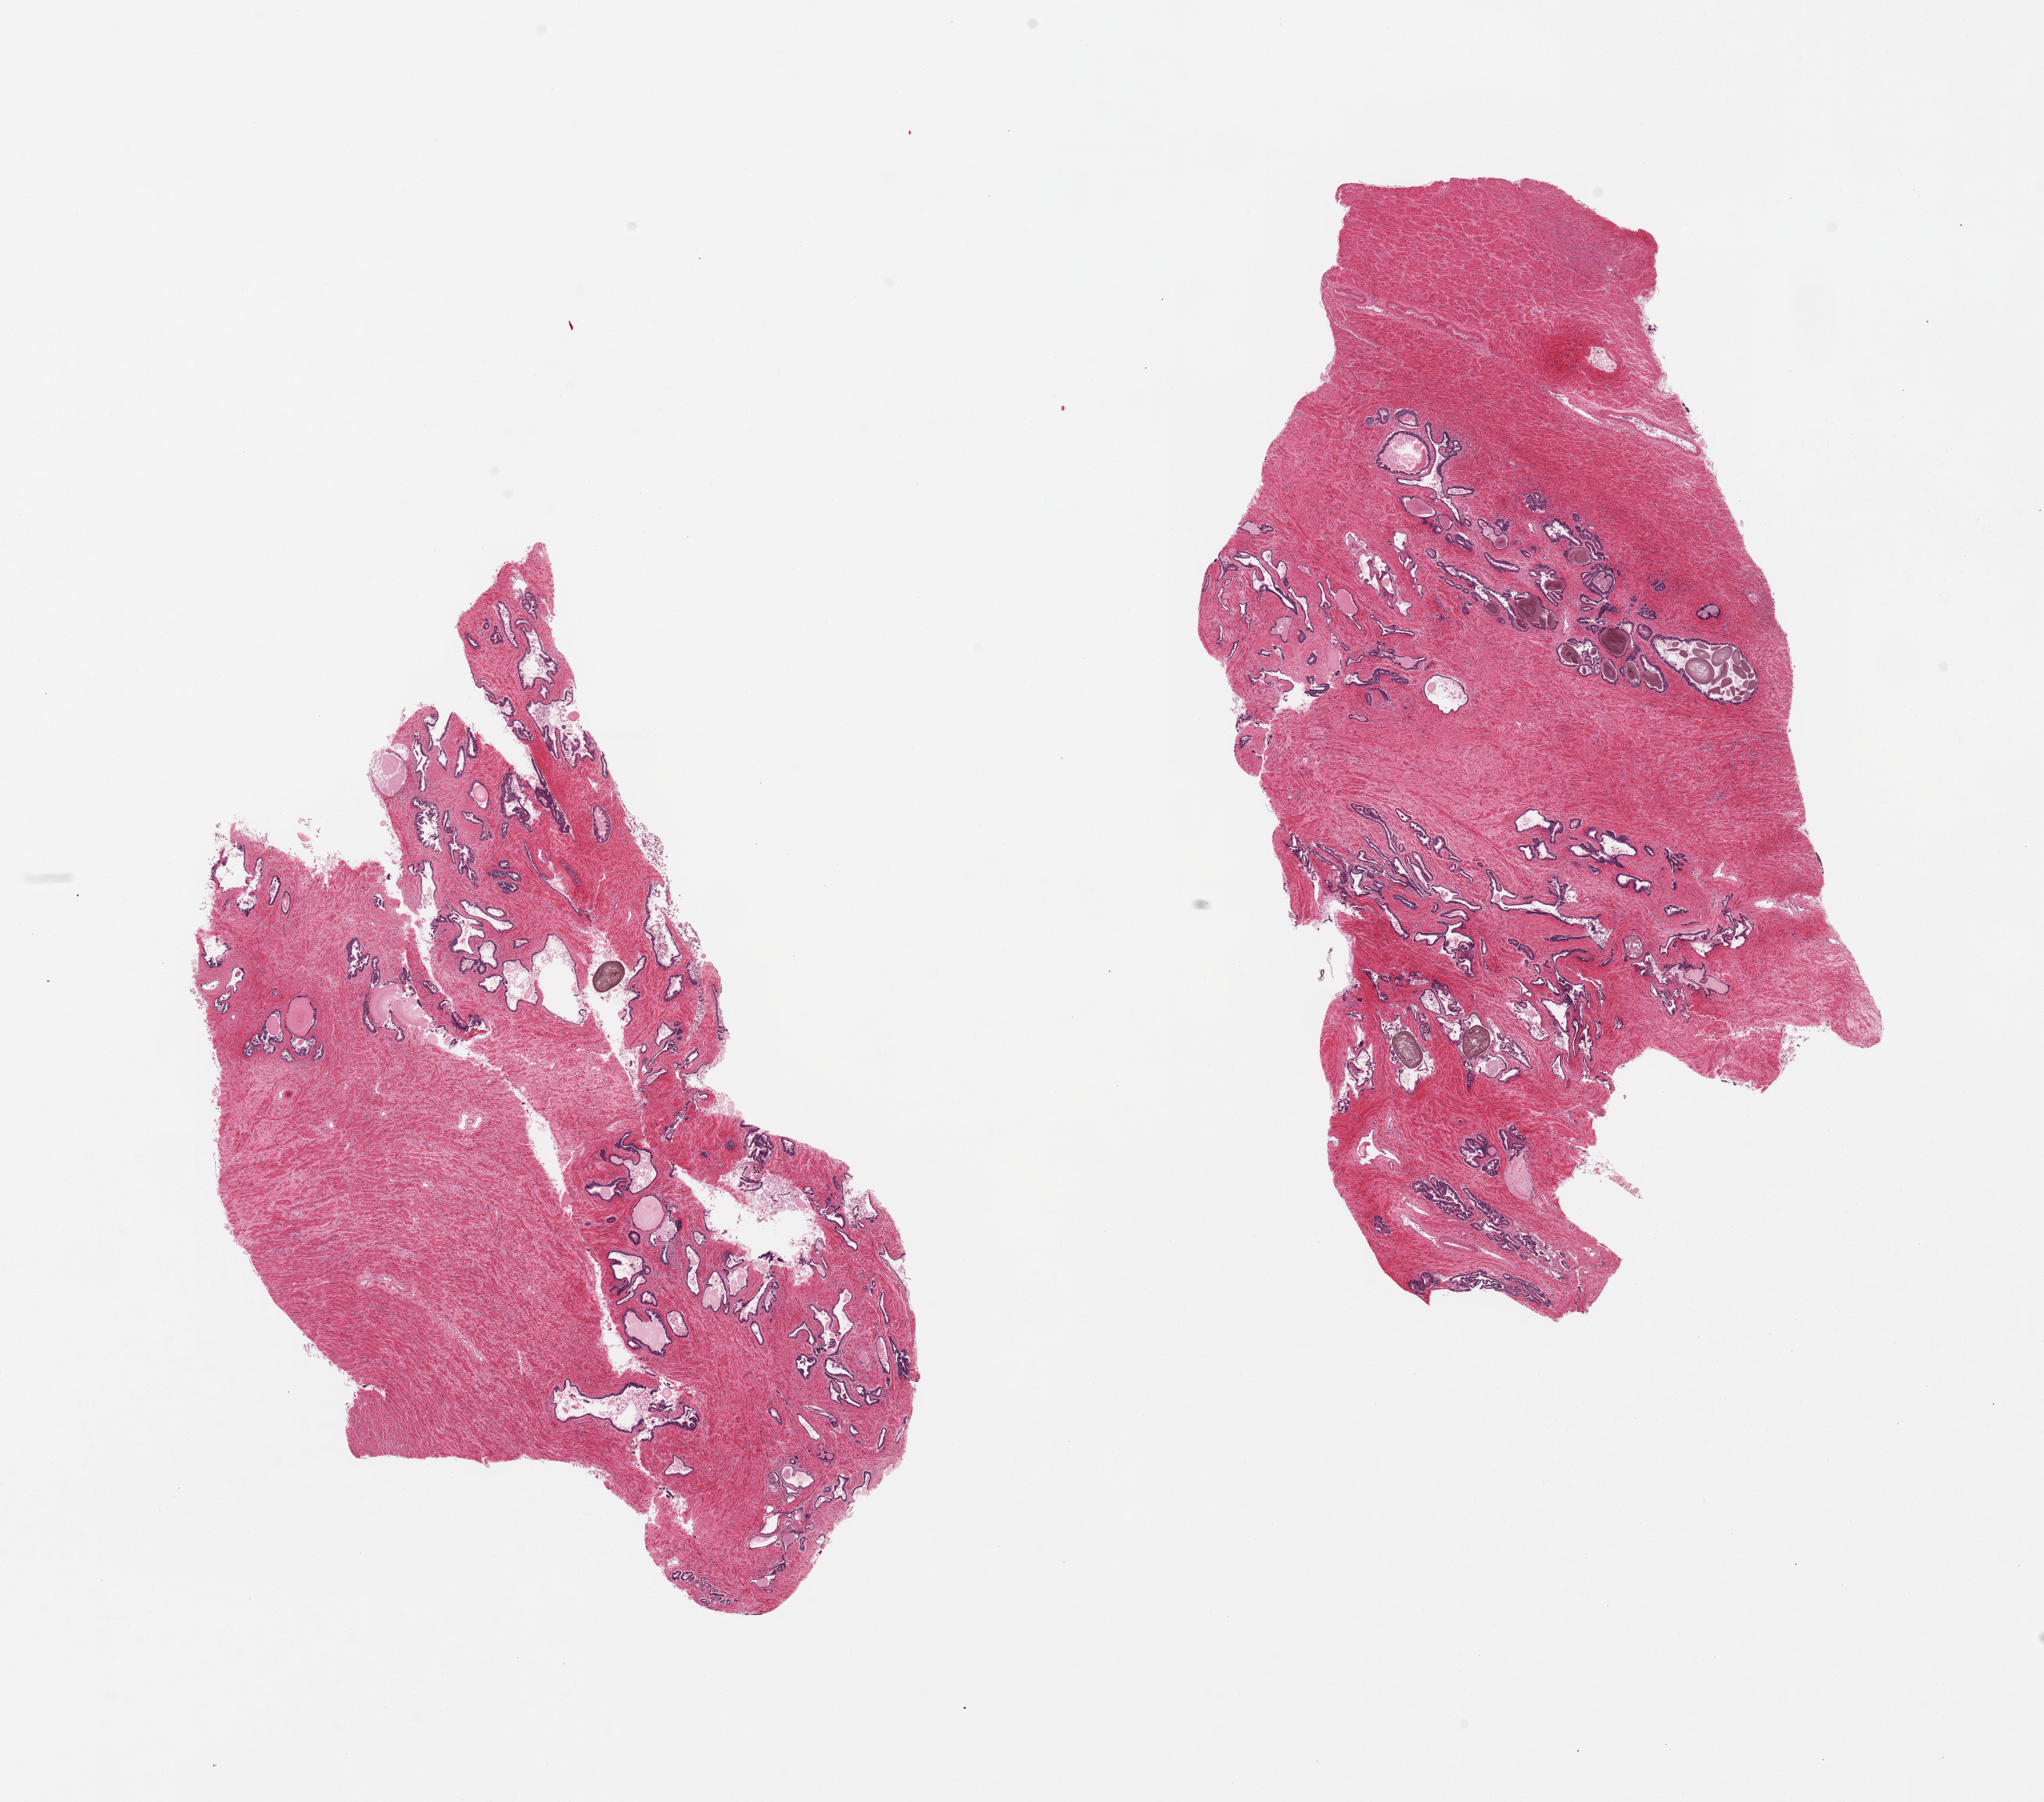
Whole-slide image, haematoxylin and eosin stain — whole scanned area (about 20.7 x 18.2 mm, slide scanned at 20x) shown as a low-resolution overview; PAXgene-fixed paraffin-embedded (PFPE) section; section of prostate (target tissue); donor tissue sample. Donor: male.
Pathologist's review note for this sample: 2 pieces.